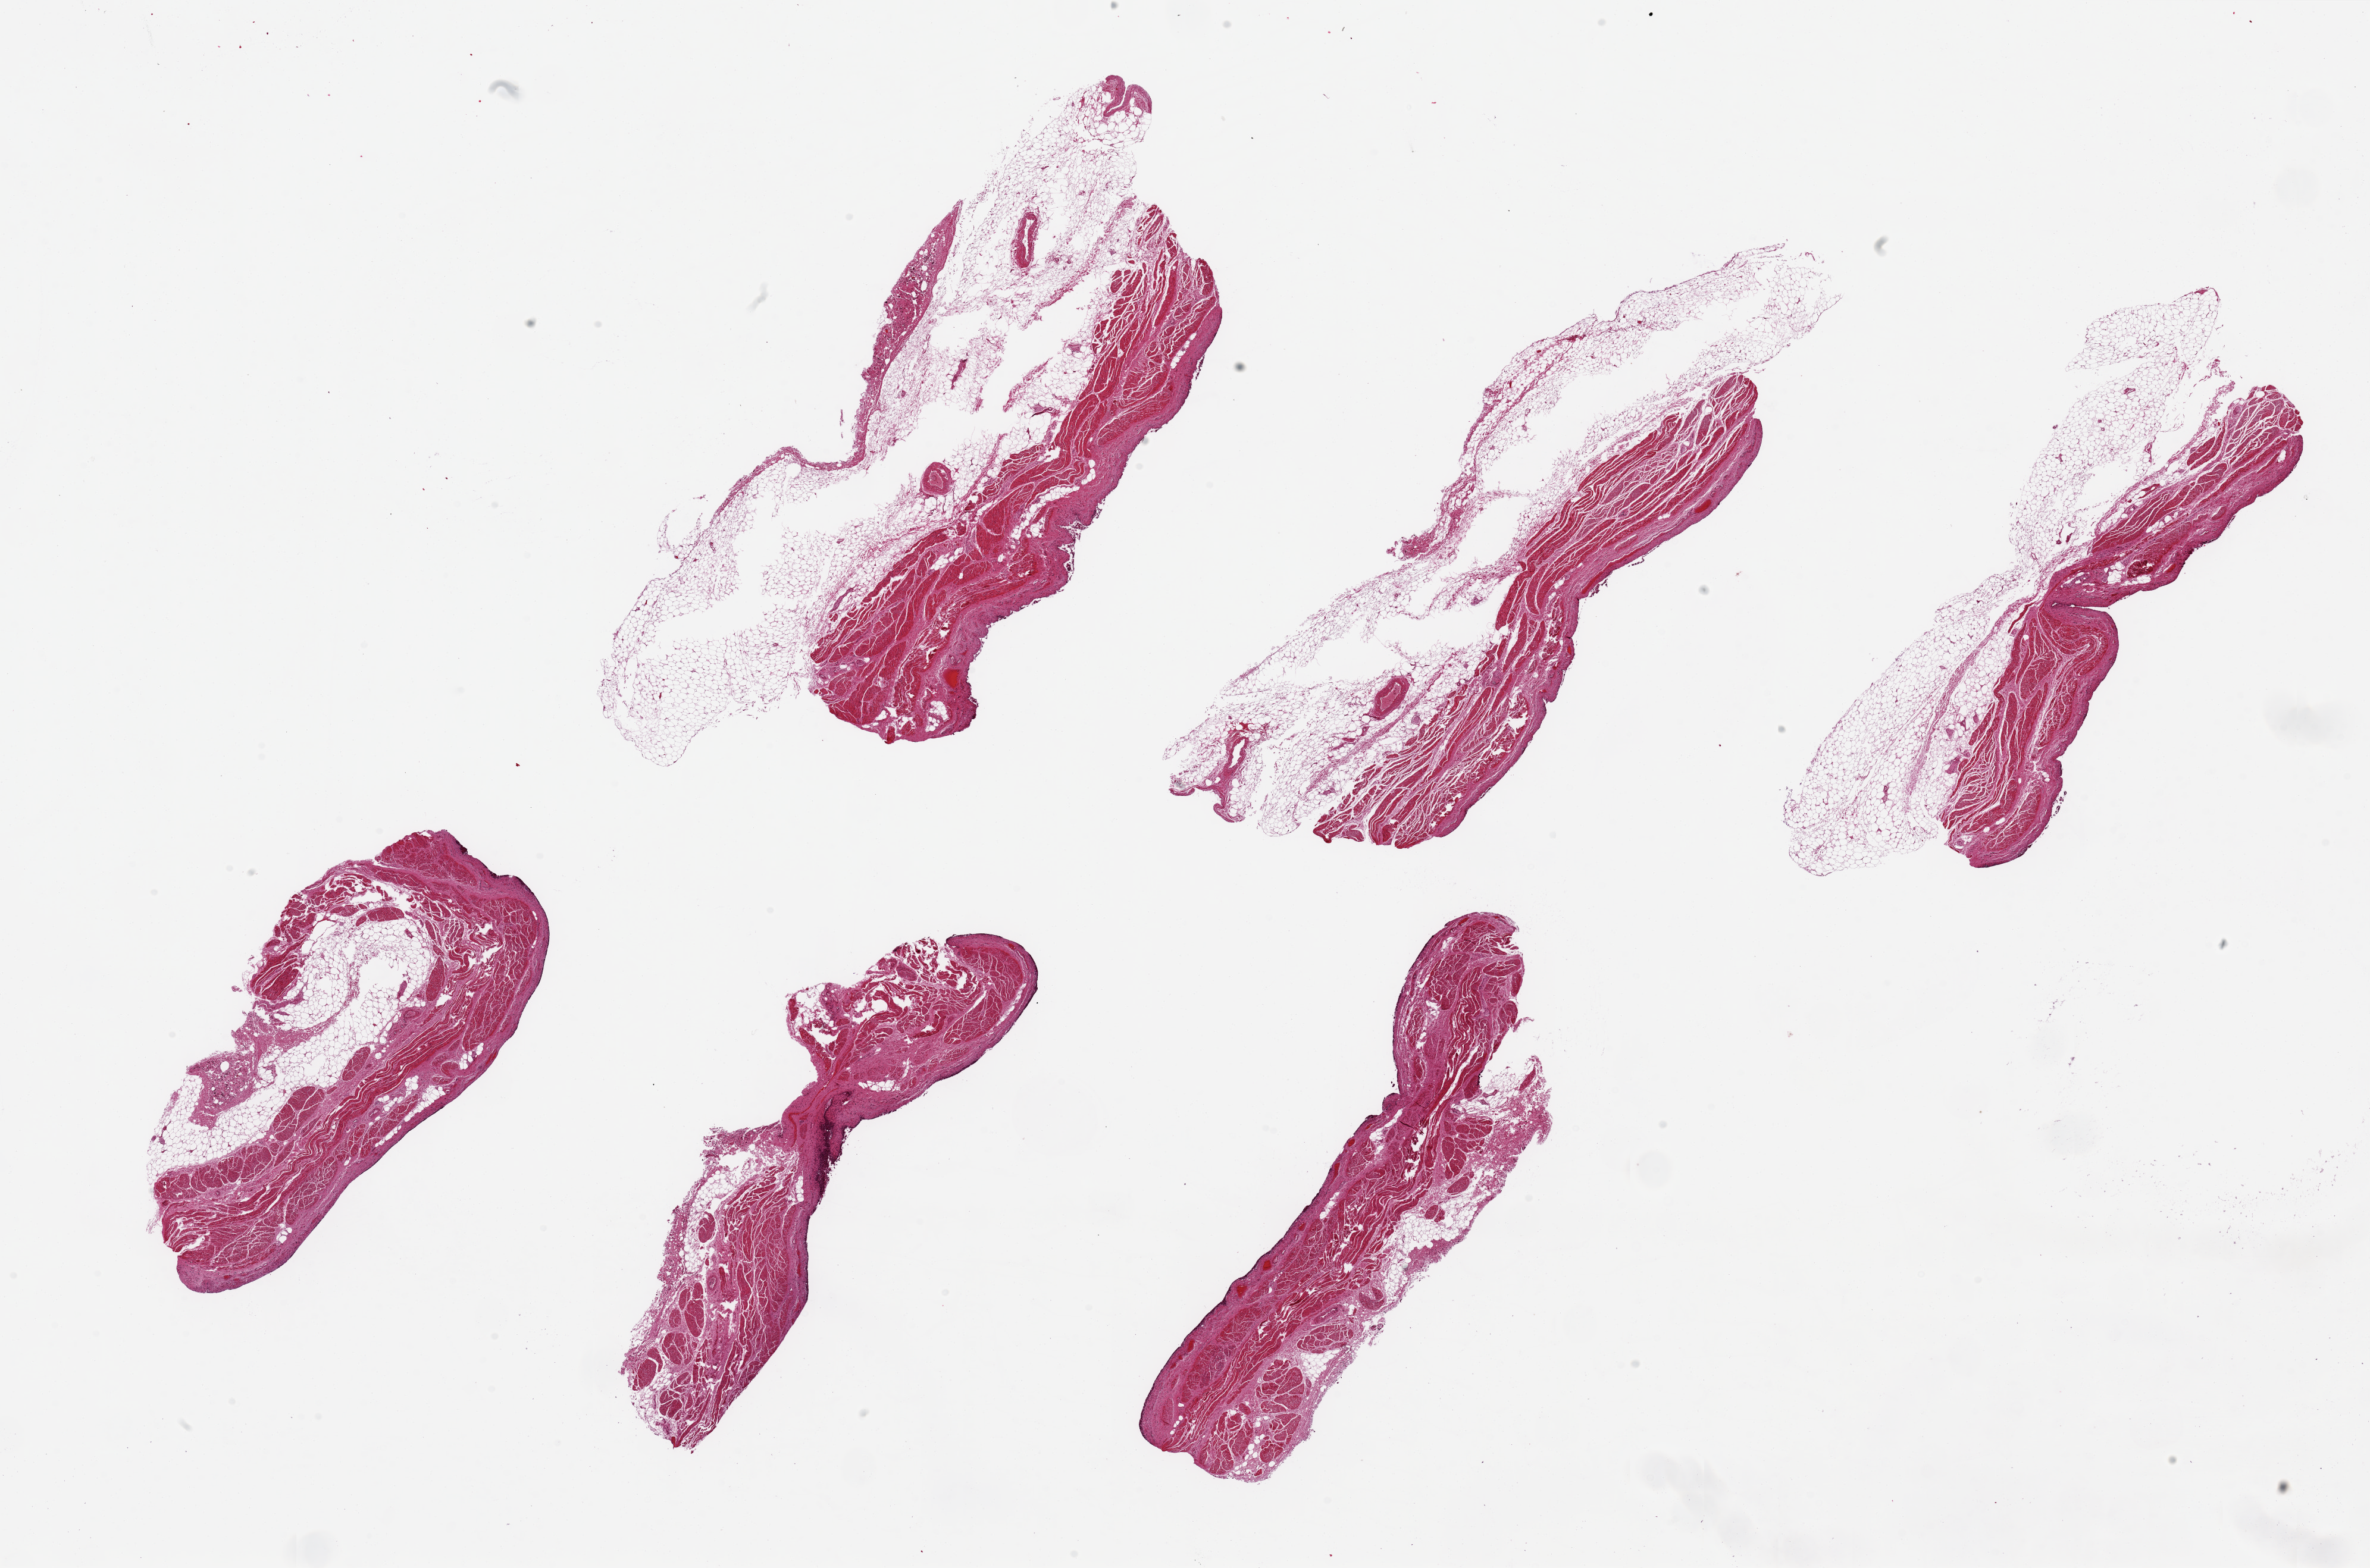
Whole-slide image, haematoxylin and eosin stain — low-resolution overview of the scanned area, about 31.5 x 20.8 mm (acquisition: 20x scan). PAXgene-fixed, paraffin-embedded tissue. Section of urinary bladder (target tissue). Donor tissue sample. Donor sex: male.
- reviewer comment on this tissue sample: 6 pieces ~8x4mm; urothelium completely sloughed, half the pieces have layer of fat up to 50% of total thickness of specimen; representative fatty areas